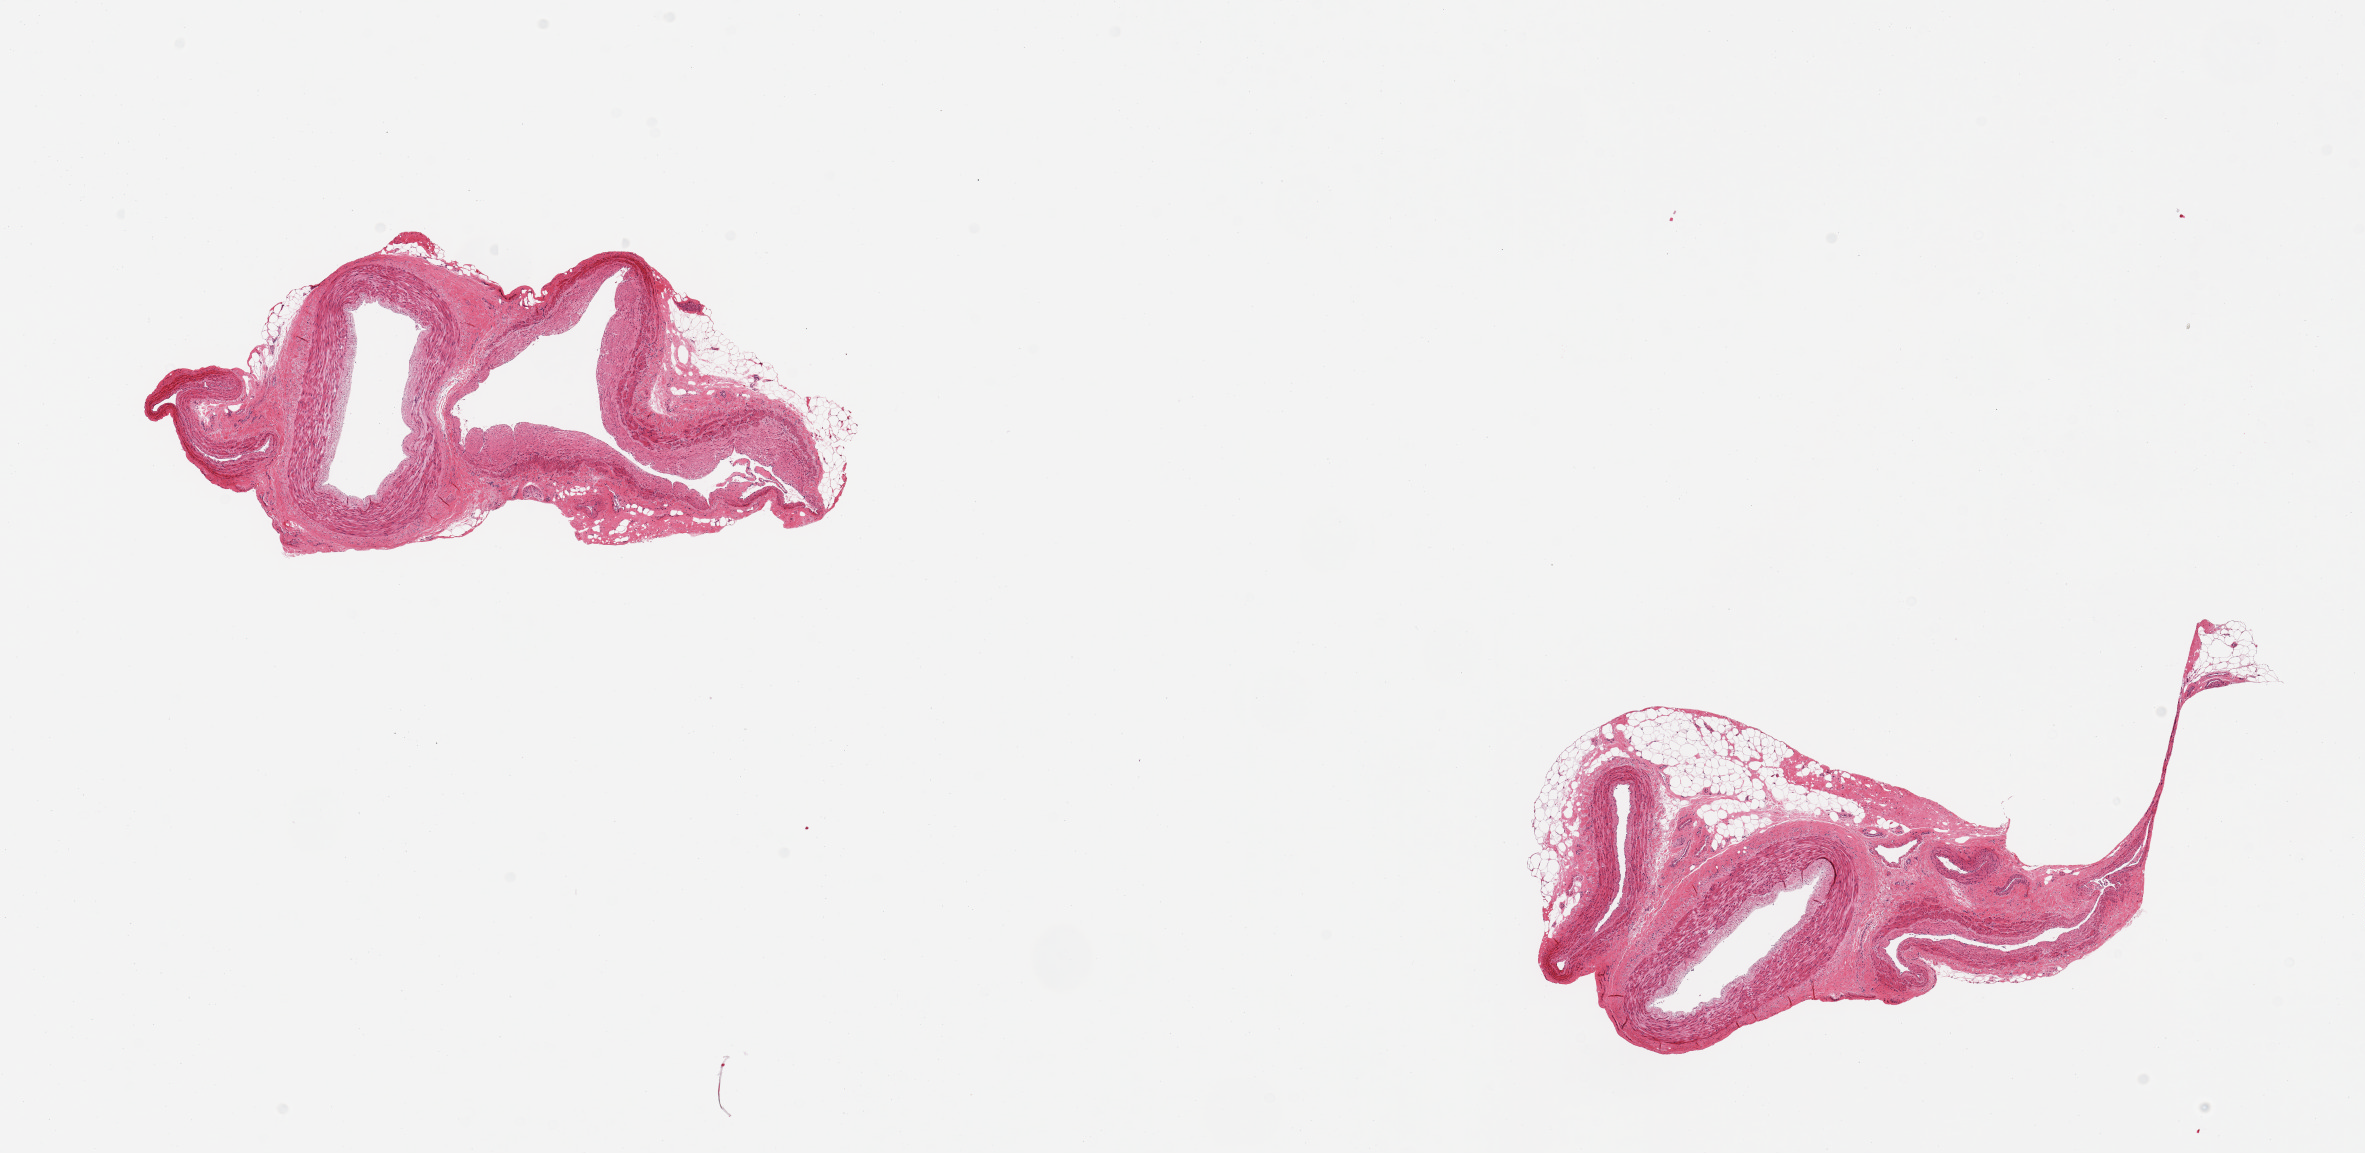
Digitized hematoxylin and eosin (H&E)-stained section, whole scanned area (about 18.7 x 9.1 mm, slide scanned at 20x) shown as a low-resolution overview; PAXgene-fixed, paraffin-embedded tissue; target tissue: tibial artery; donor tissue sample. Donor sex: female.
Pathologist's review note for this sample: 2 pieces; includes adjacent vein and attached fat (1.3mm).